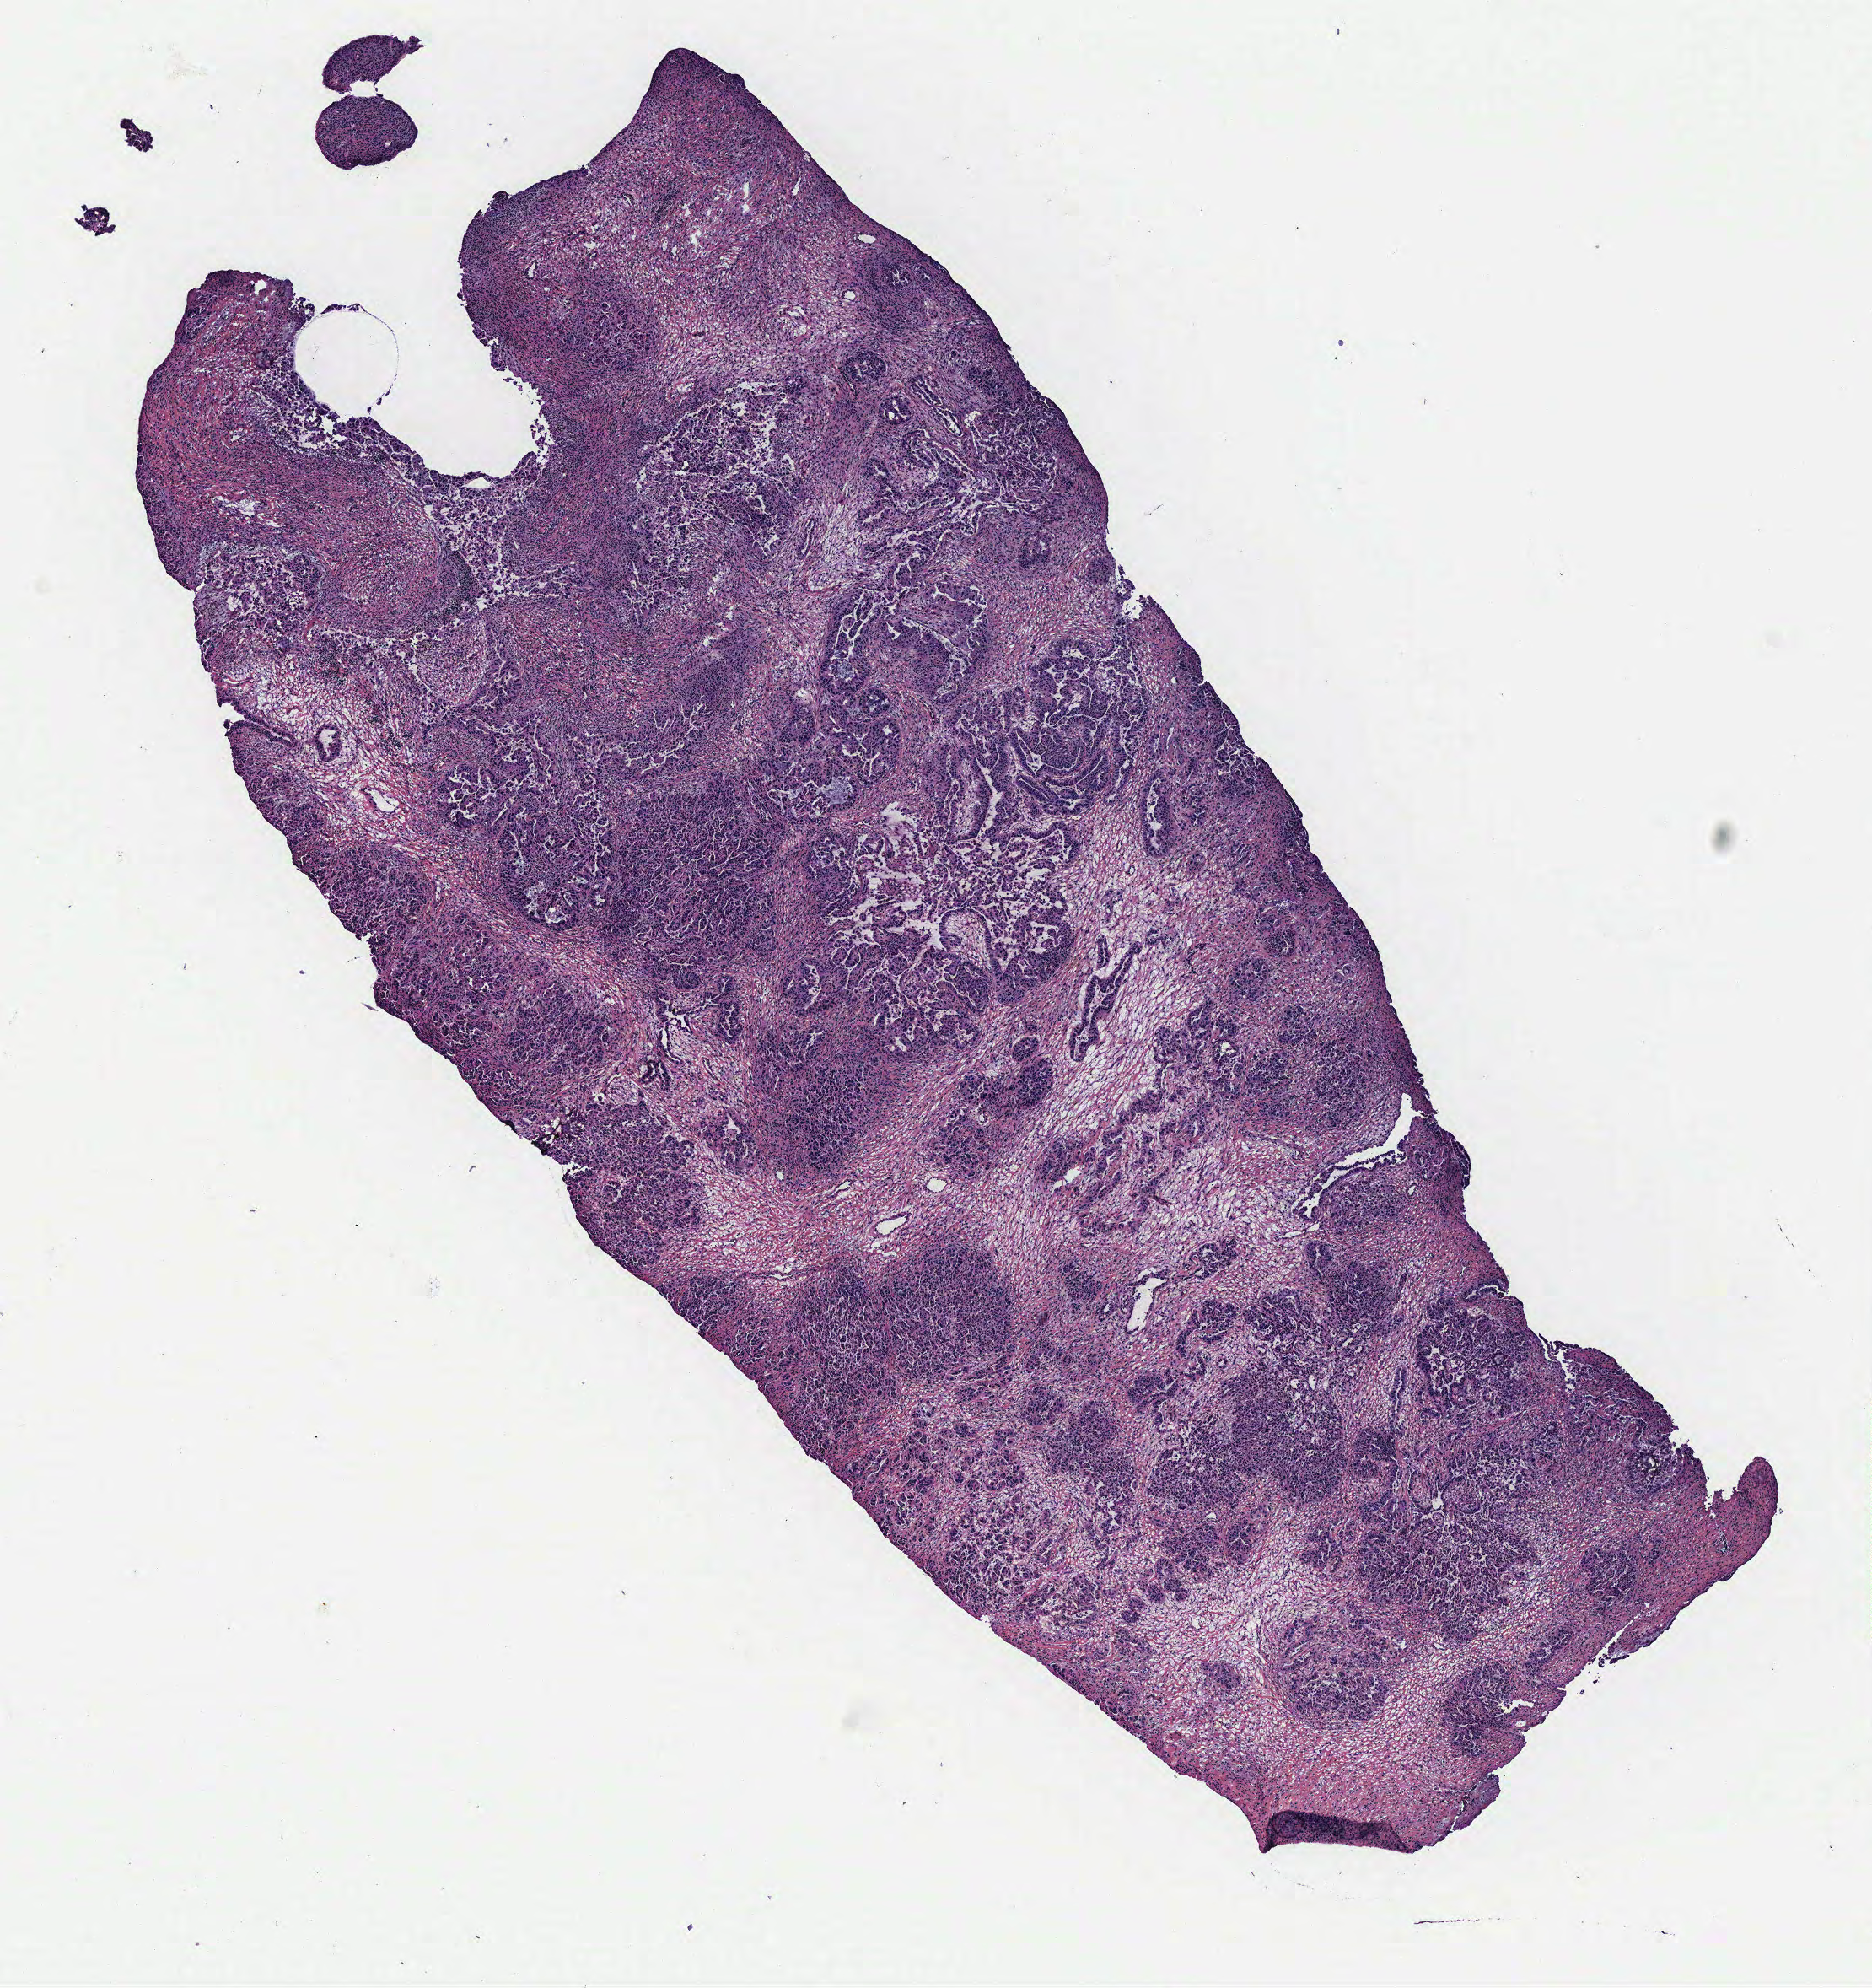
Digitized H&E tissue section (whole slide) — whole scanned area (about 8.9 x 9.4 mm, from a 40x scan) shown as a low-resolution overview; ovary, tumour tissue. Patient: female, age 58 years.
Diagnosis: Serous adenocarcinoma, NOS. Primary tumour site (as recorded): ovary.